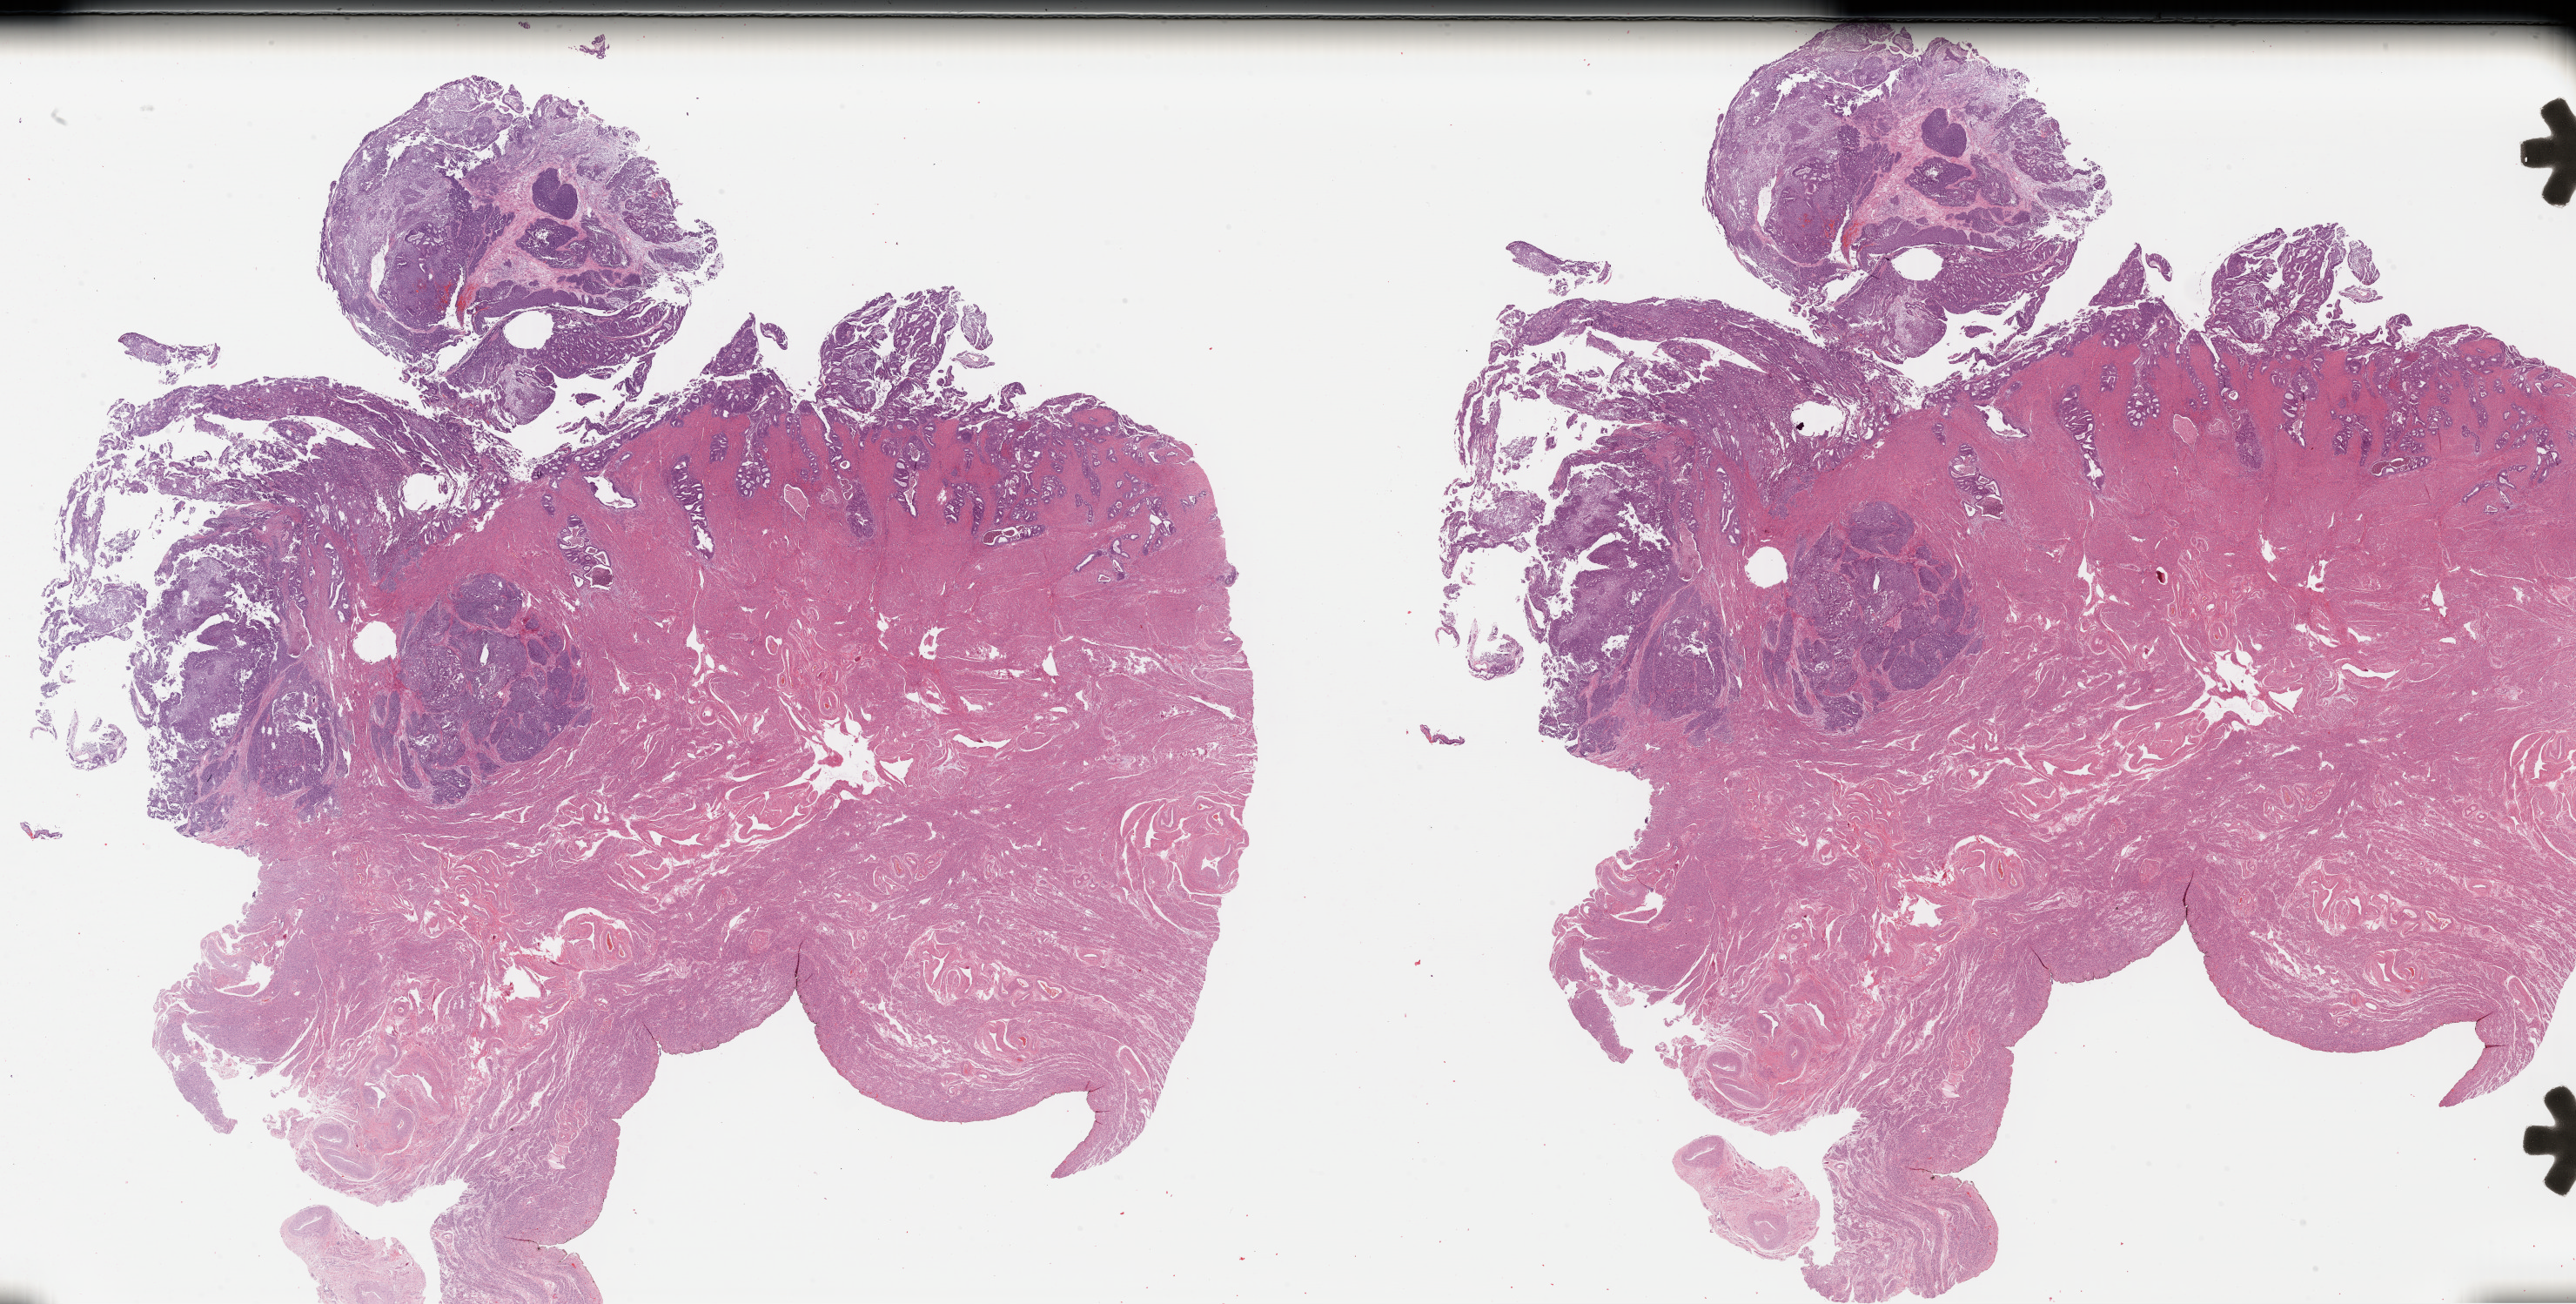
H&E whole-slide image, shown as a low-resolution overview of the whole scanned area (about 46.5 x 23.5 mm, slide scanned at 40x), FFPE section, sample: primary tumour, uterus. Female patient; age at initial diagnosis 74 years.
Histologic diagnosis: Mullerian mixed tumor (endometrium).